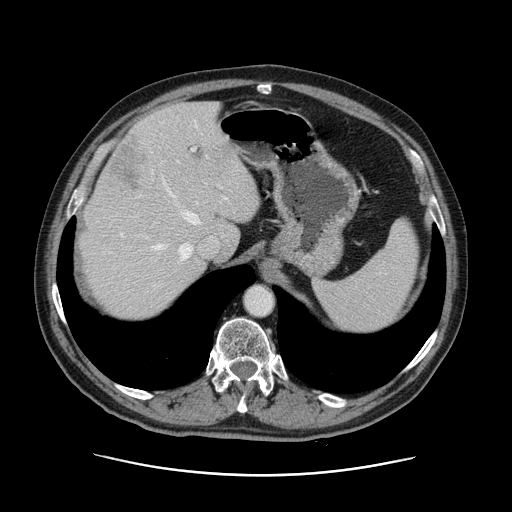
Contrast-enhanced abdominal CT, one axial slice. Position 97 of 141 along the scan axis. 120 kVp. Intravenous contrast given. Soft-tissue window (W 400 / L 40 HU). 512 × 512 image matrix, field of view 395 × 395 mm. Male patient, age 72 years. Case-level facts recorded for this patient, not image findings: diagnosis: colorectal cancer liver metastases, imaged before liver resection; multiple liver metastases: yes; largest metastasis: 5.4 cm; disease in both lobes: yes.
Annotated regions visible in this slice (manually delineated by an expert):
- hepatic veins: box from (x=121, y=122) to (x=207, y=260) px
- liver: (x=79, y=102)–(x=260, y=322)
- planned liver remnant (the part of the liver to remain after resection): (x=81, y=102)–(x=260, y=322)
- portal vein (with intrahepatic branches): (x=181, y=148)–(x=228, y=255)
- liver metastasis: (x=107, y=131)–(x=150, y=193)